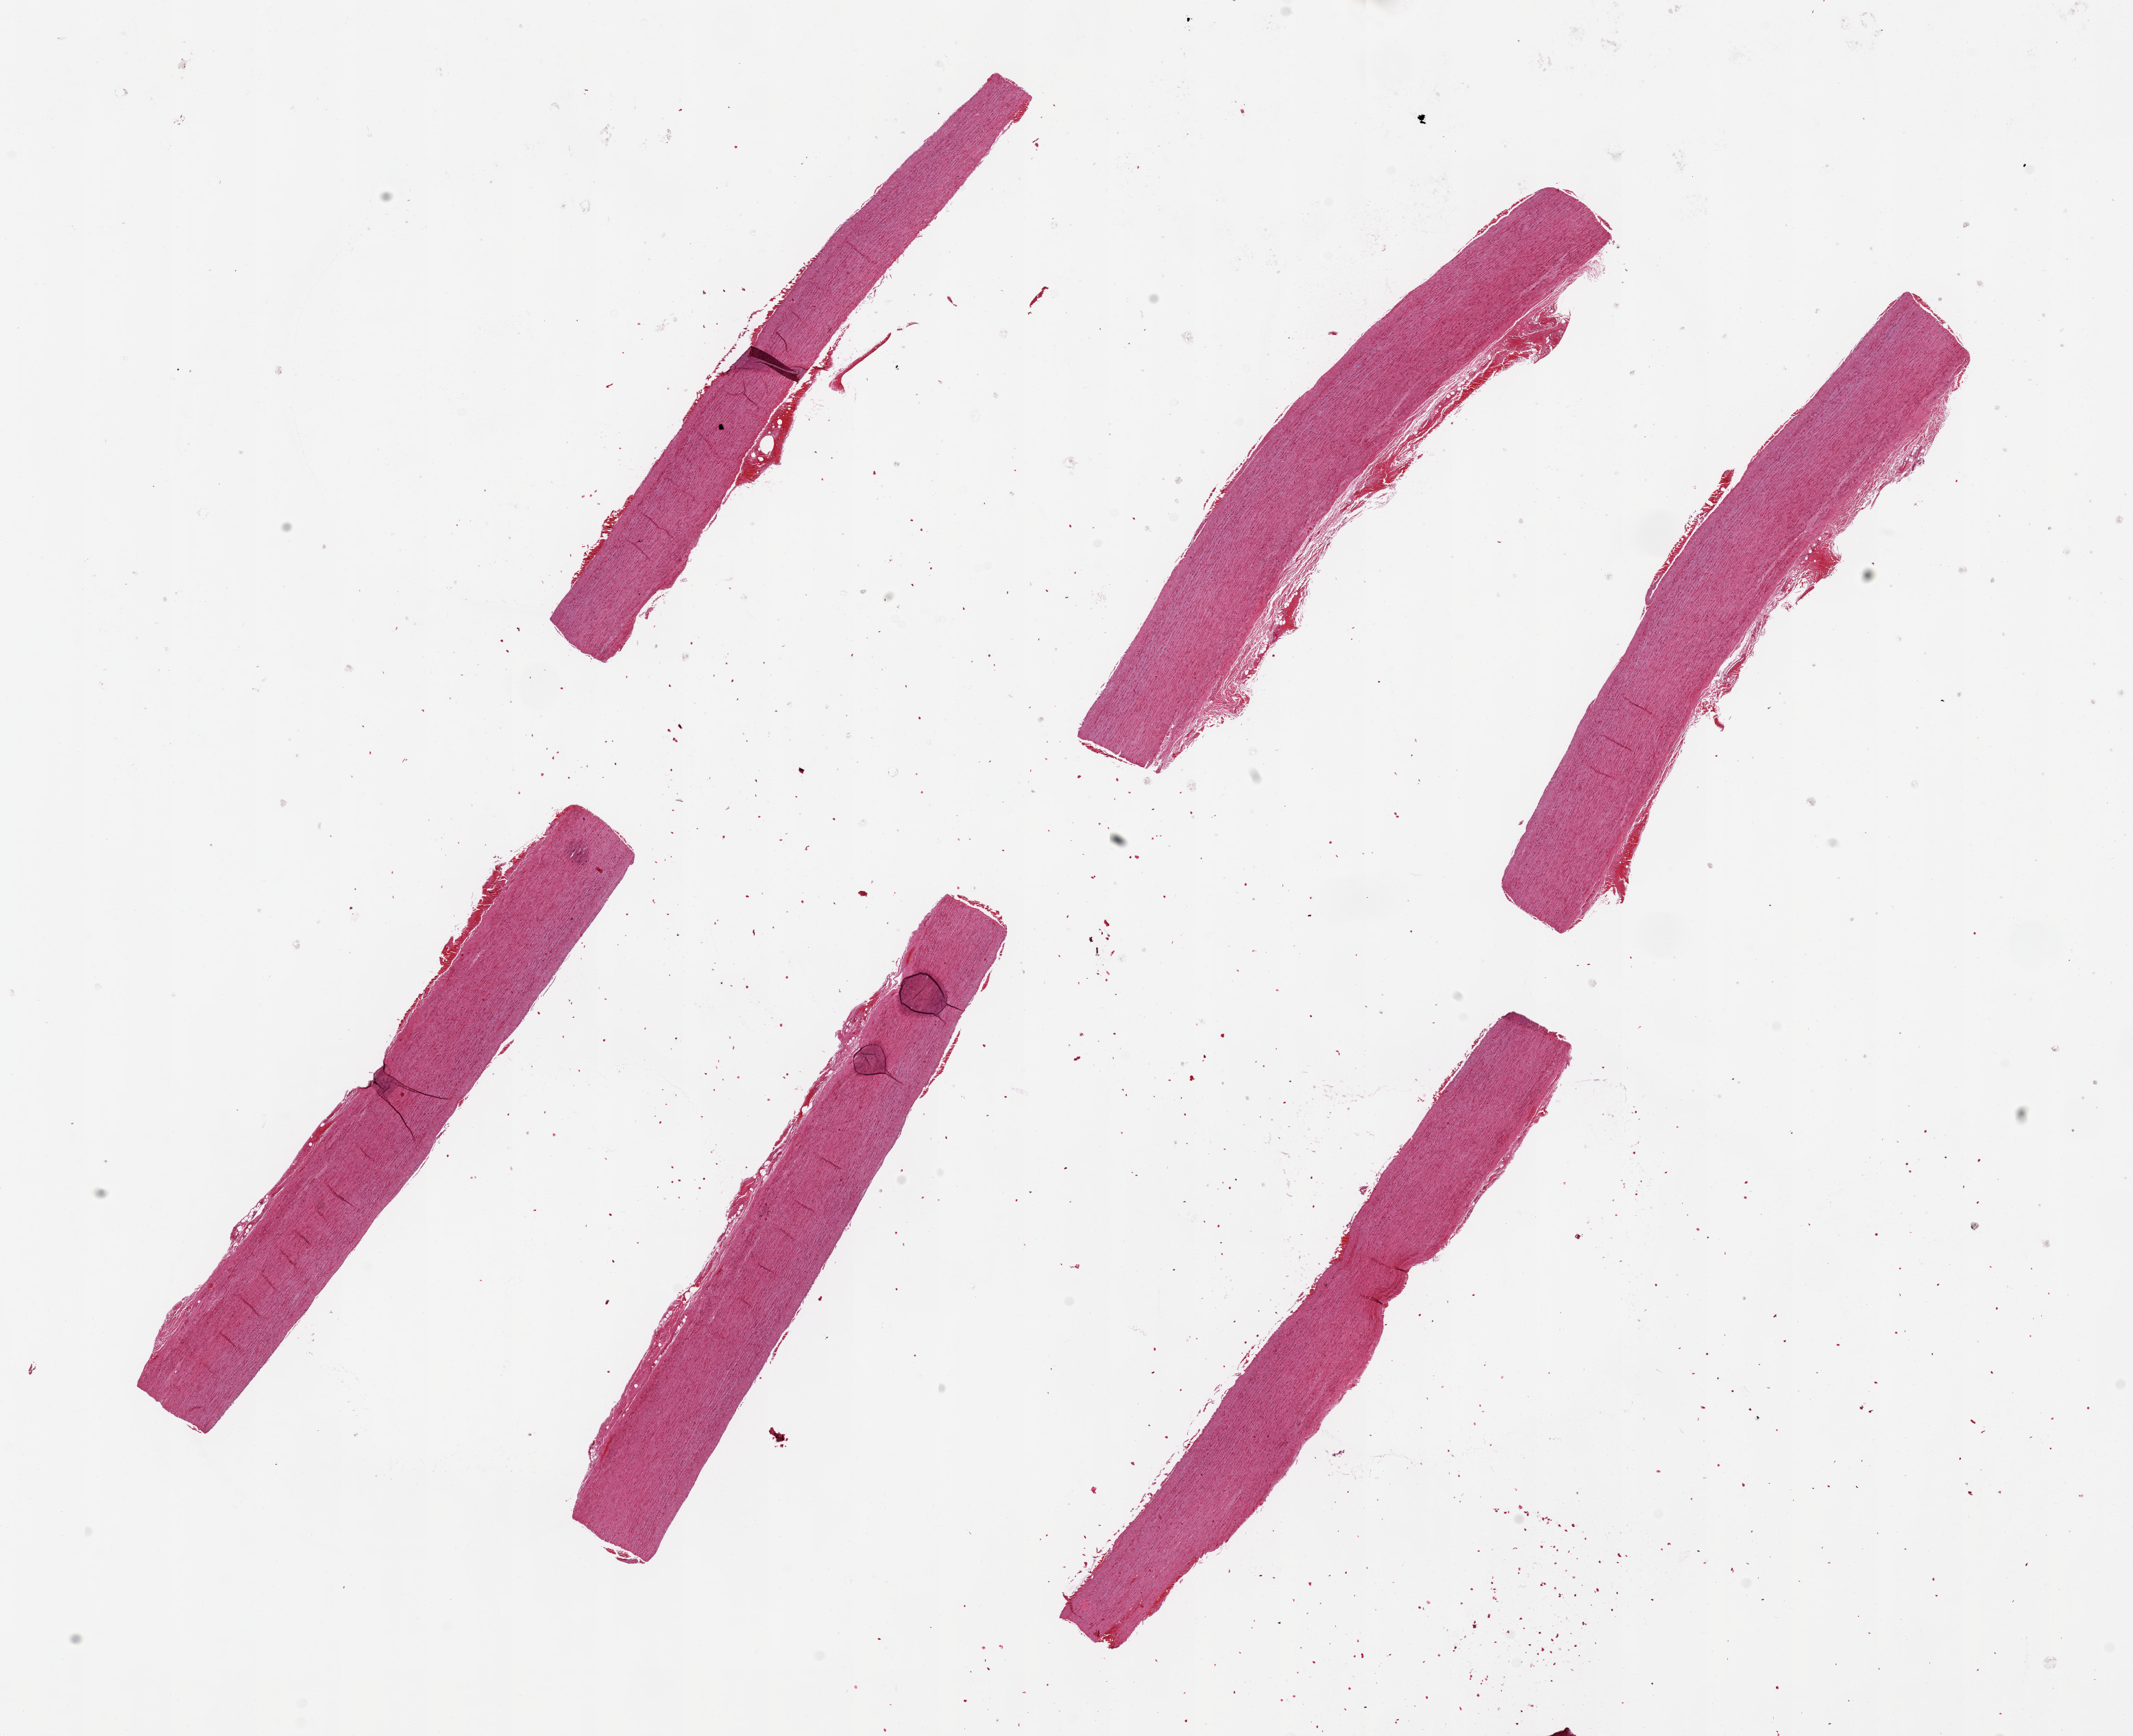
Digitized H&E-stained section — low-resolution overview of the scanned area, about 24.6 x 20.0 mm (acquisition: 20x scan), PAXgene-fixed, paraffin-embedded tissue, target tissue: aorta, tissue donor sample. Donor sex: male.
Pathologist's review note for this sample: 6 pieces, up to 9x1mm; minimal atherosis.